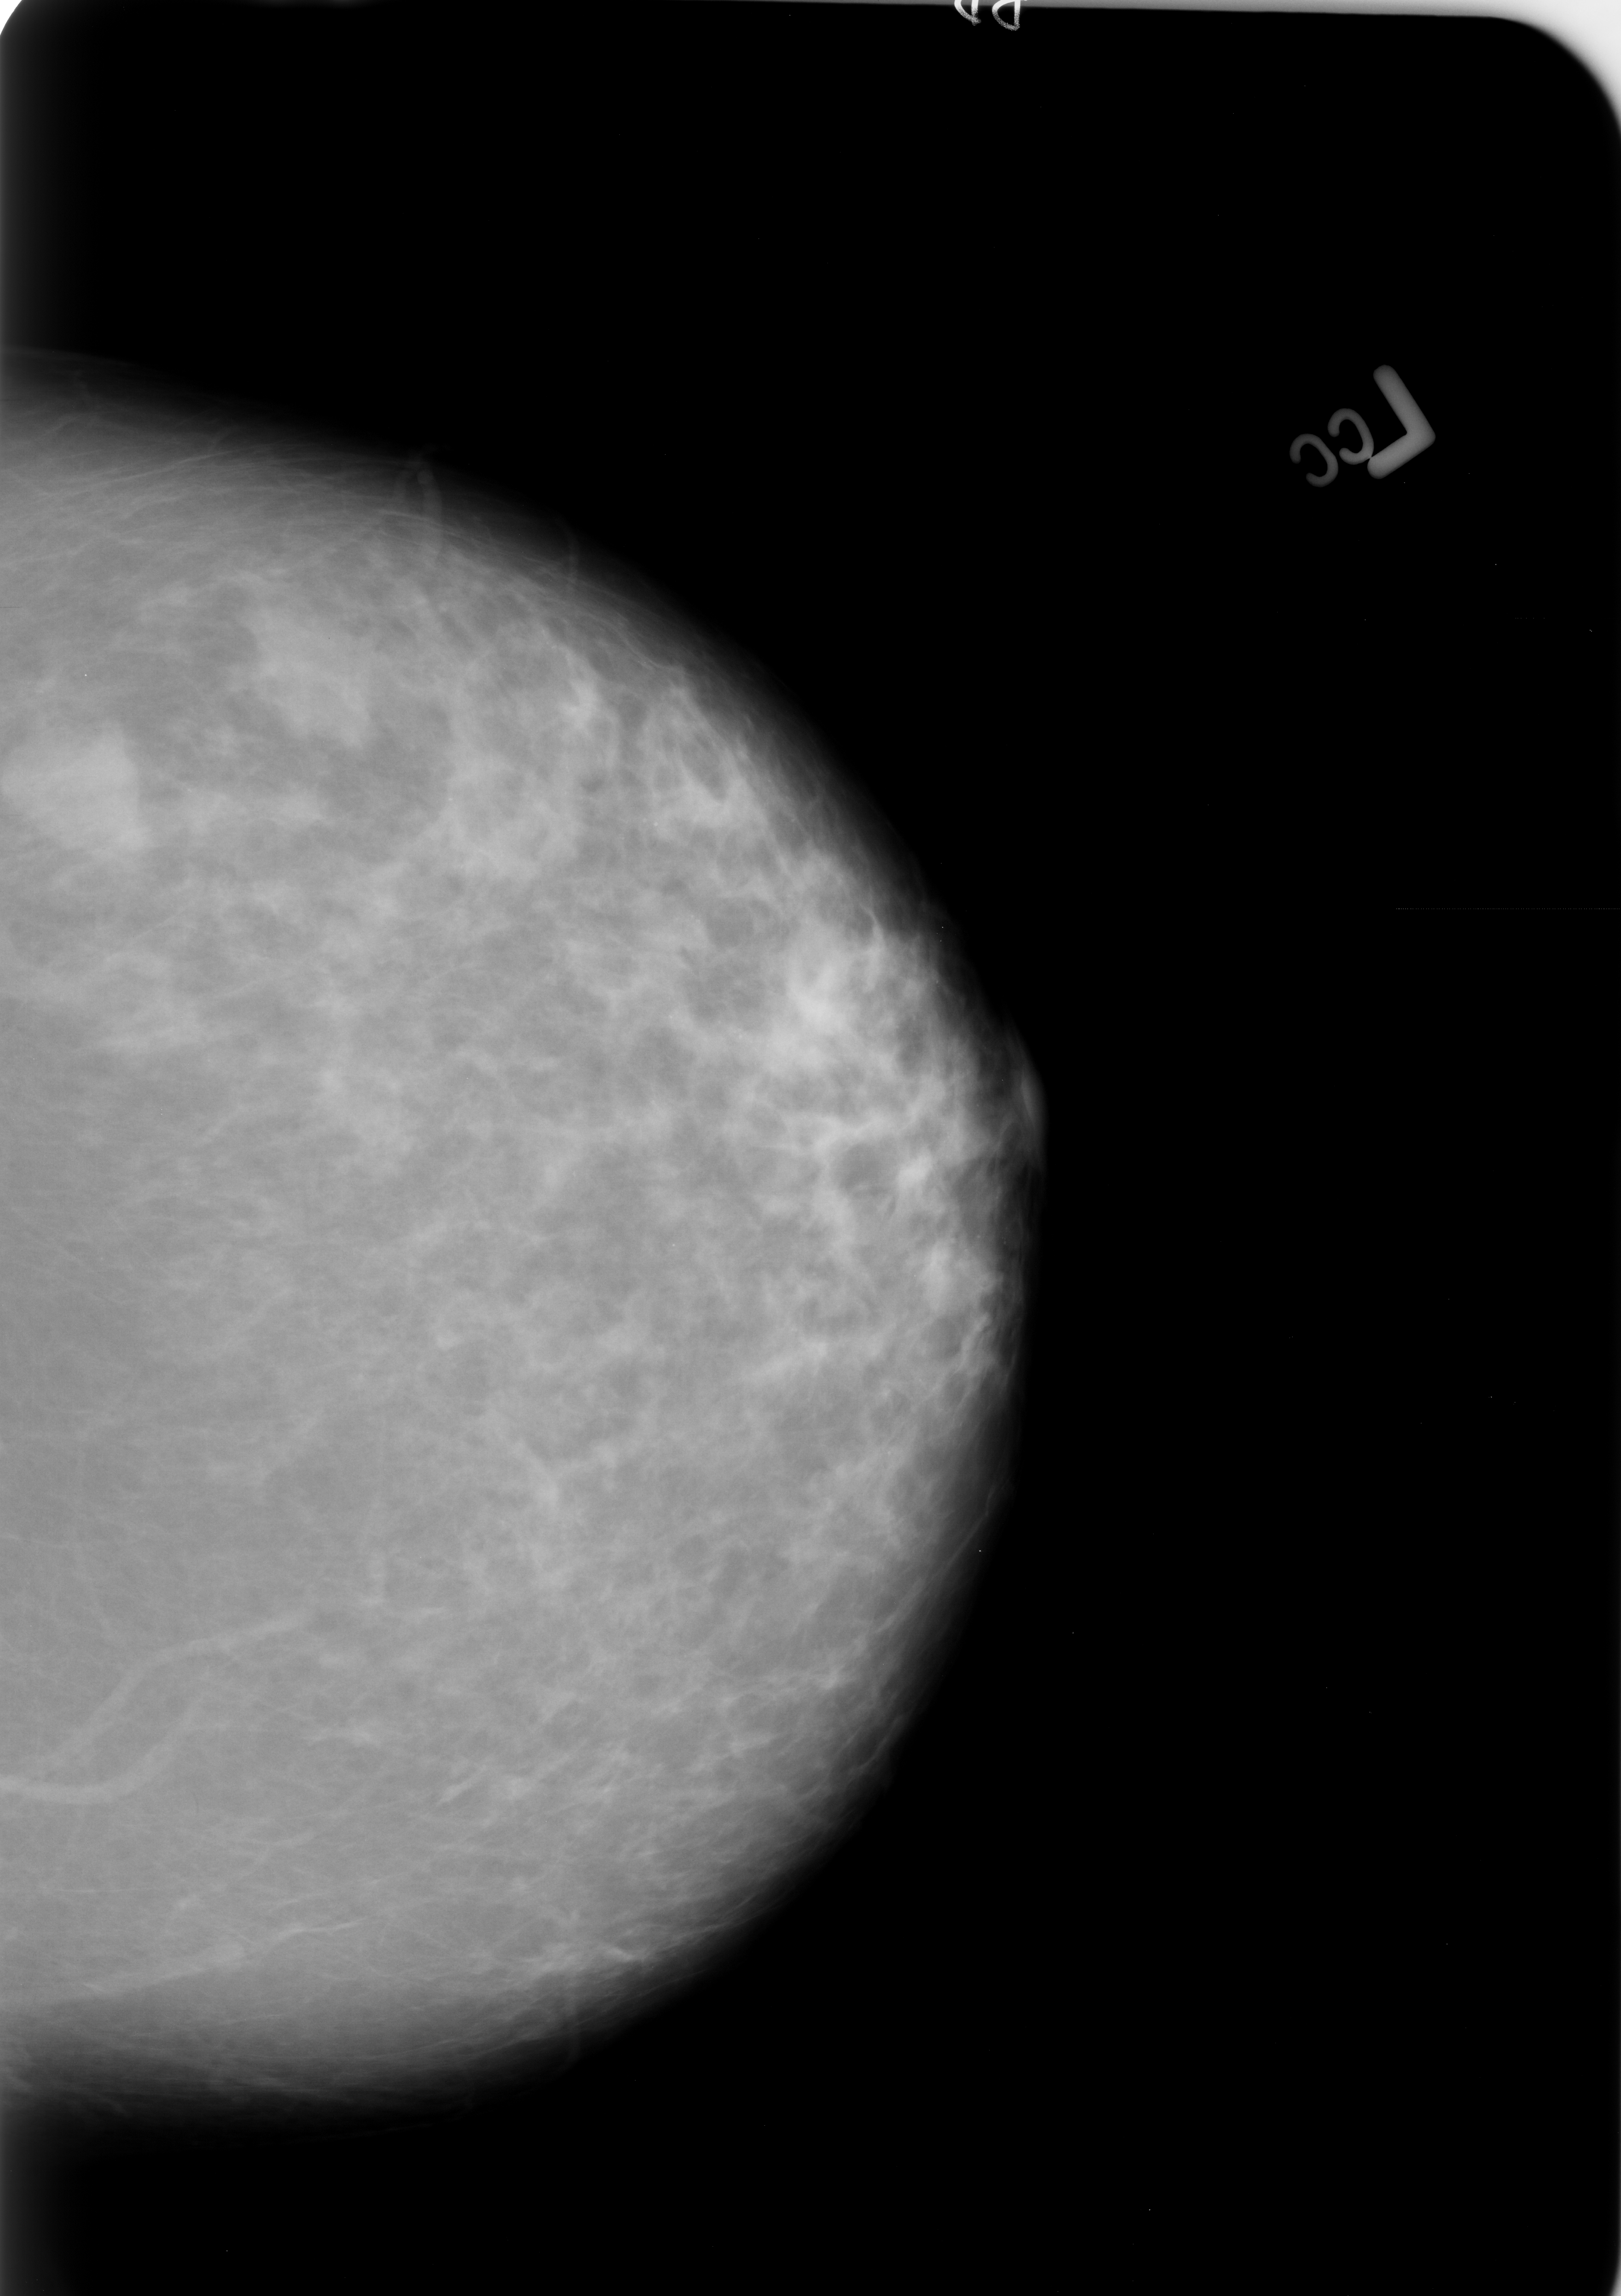
Mammogram (digitized film), left breast, craniocaudal (CC) view, BI-RADS breast density category 2 (scale 1–4).
Radiologist-marked abnormalities on this image: mass, shape lobulated, margins circumscribed; BI-RADS assessment category 4; subtlety rating 5 on a 1 (subtle) to 5 (obvious) scale; pathology result (as recorded, not read from the image): benign.